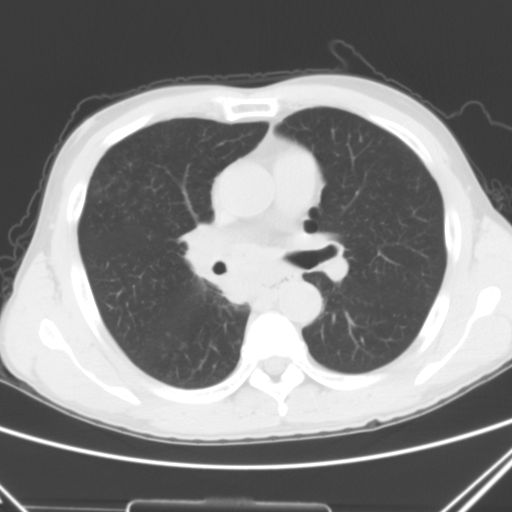
Chest CT, one axial slice. Slice 27 of 51 in the series (ordered by position). Lung window (W 1500 / L -600 HU). 5 mm slice thickness. 512 × 512 image matrix, field of view 327 × 327 mm. Patient: male, 52 years. Case-level facts recorded for this patient, not image findings: clinical TNM (as recorded): T2a N0 M1c.
Annotated regions visible in this slice (bounding box drawn by a radiologist):
- lung tumour (recorded histology: squamous cell carcinoma): box from (x=176, y=217) to (x=252, y=322) px